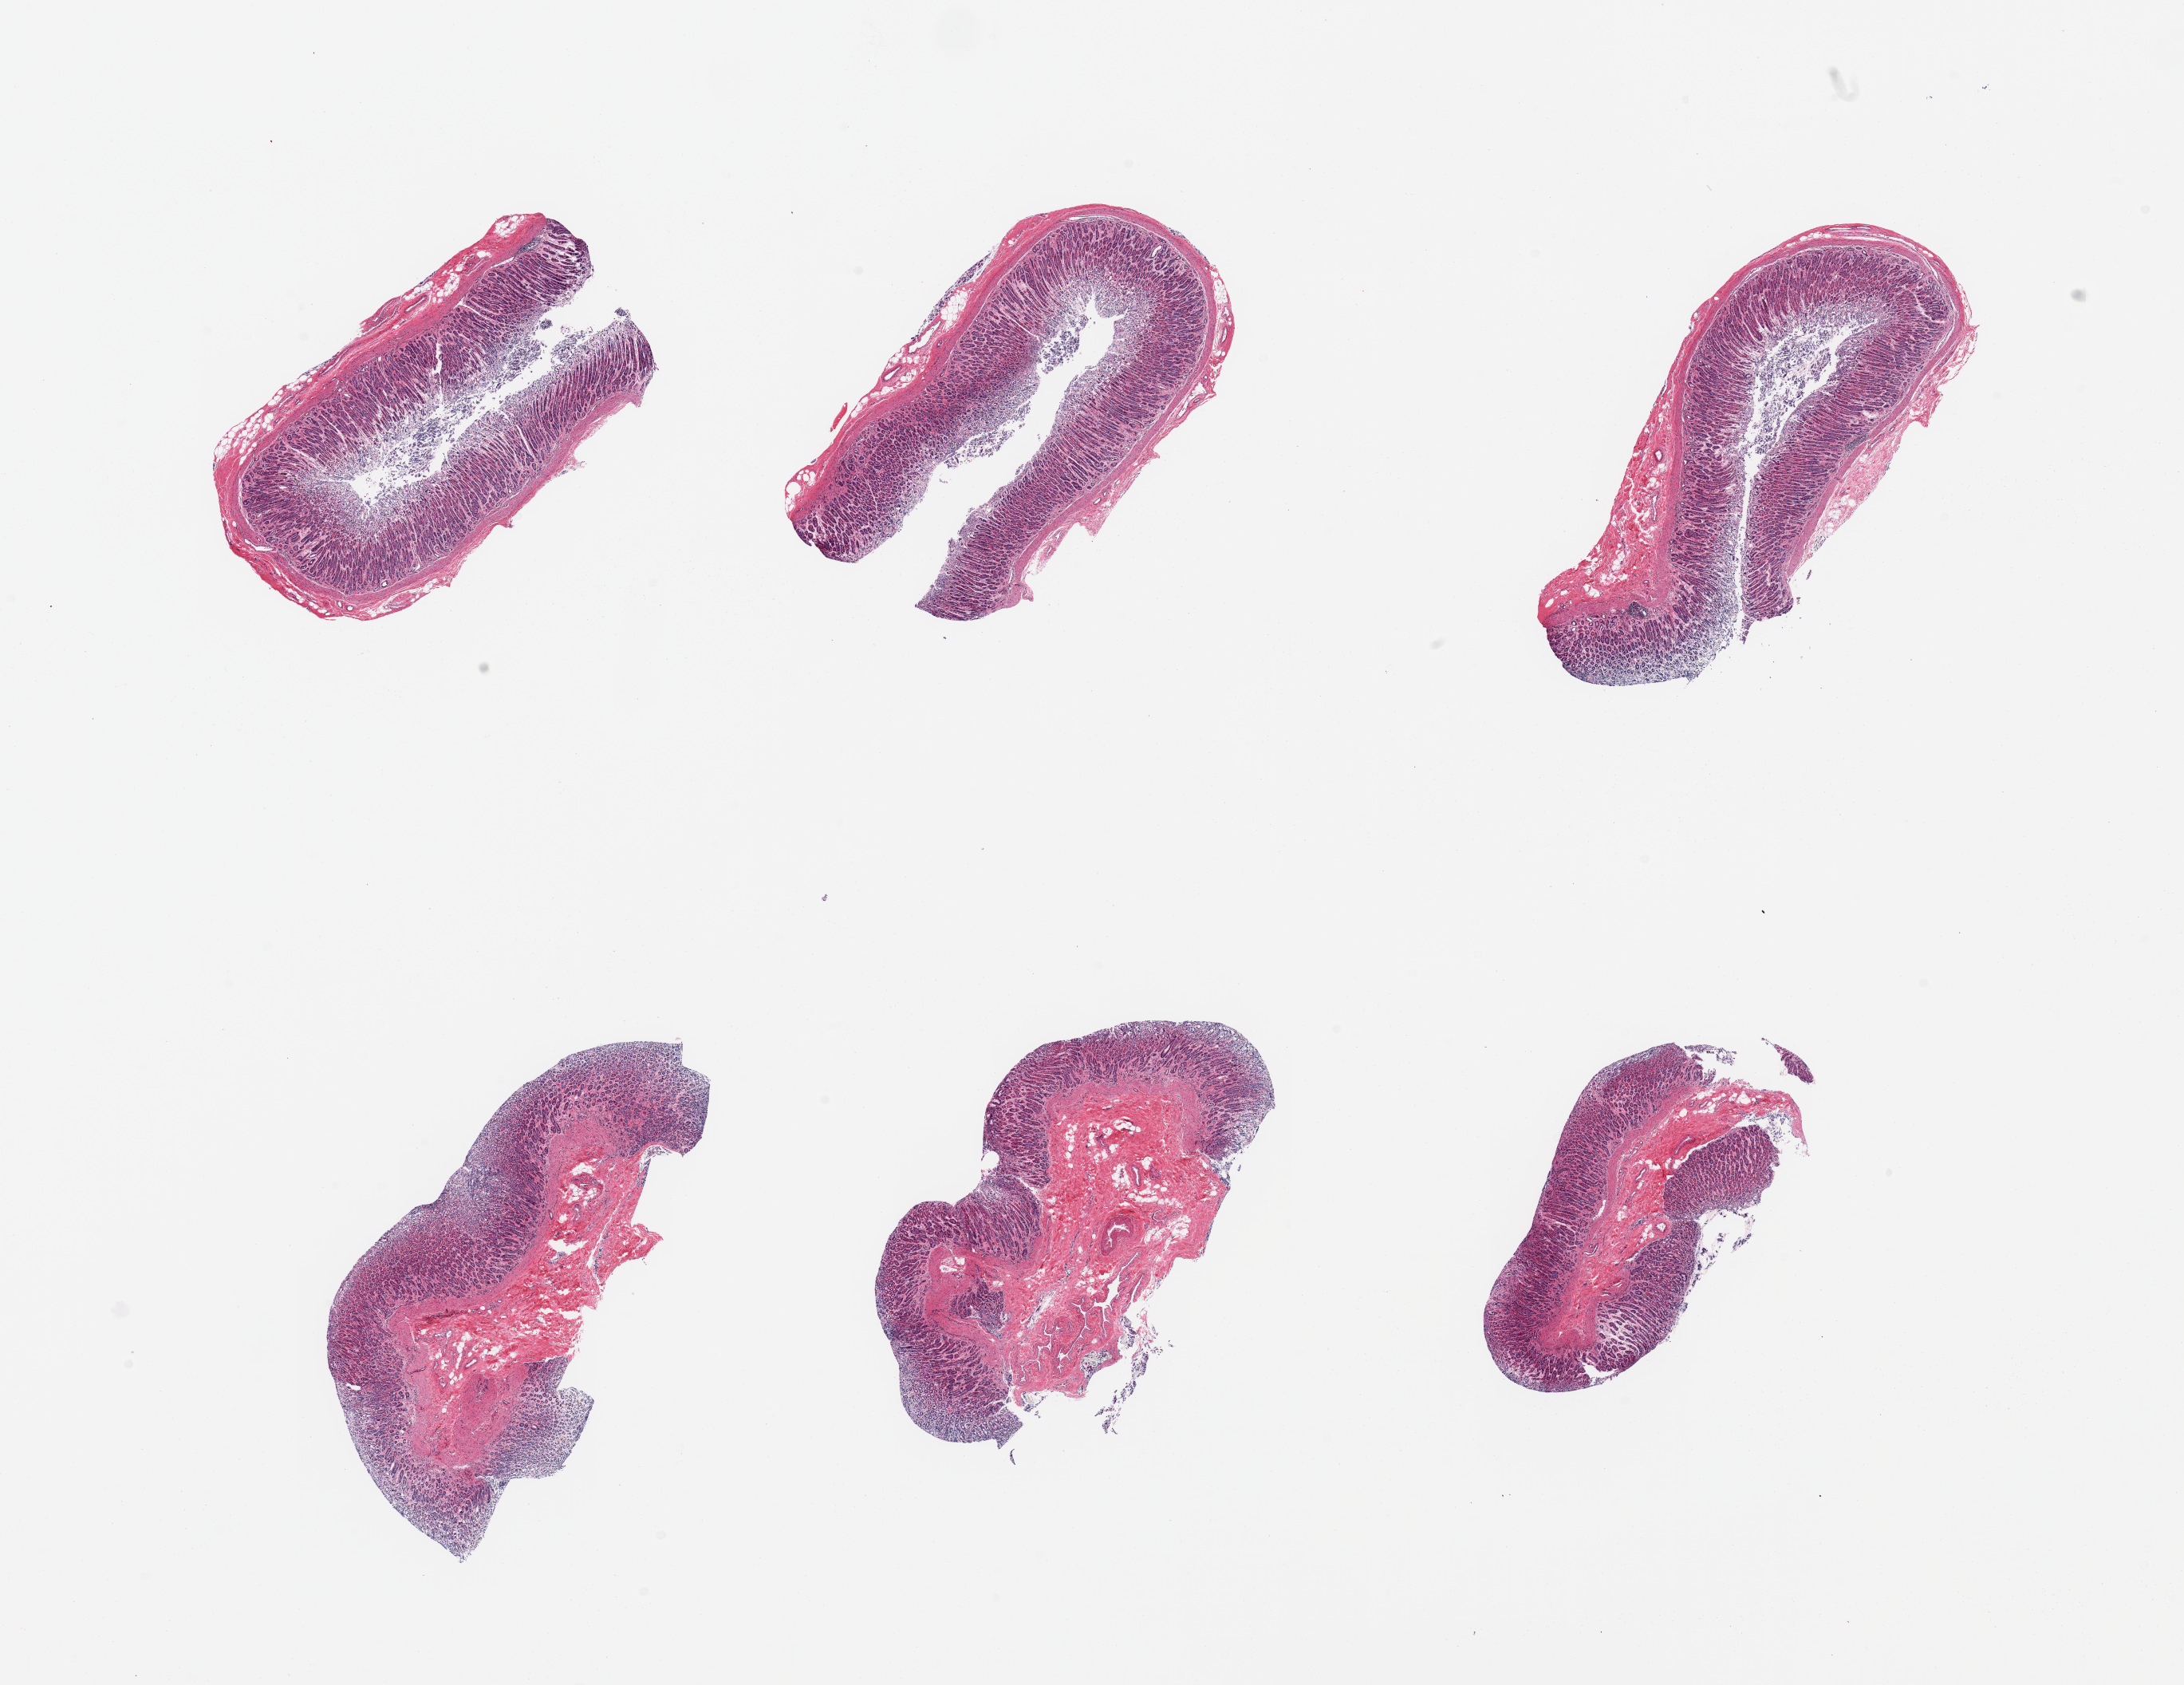
Digitized haematoxylin and eosin-stained section, brightfield, low-resolution overview of the scanned area, about 21.7 x 16.7 mm; PAXgene-fixed, paraffin-embedded tissue; sampled site (target tissue): stomach; tissue donor sample. Donor: female.
- review note (as recorded): 6 pieces; mild to moderate autolysis of gastric mucosa